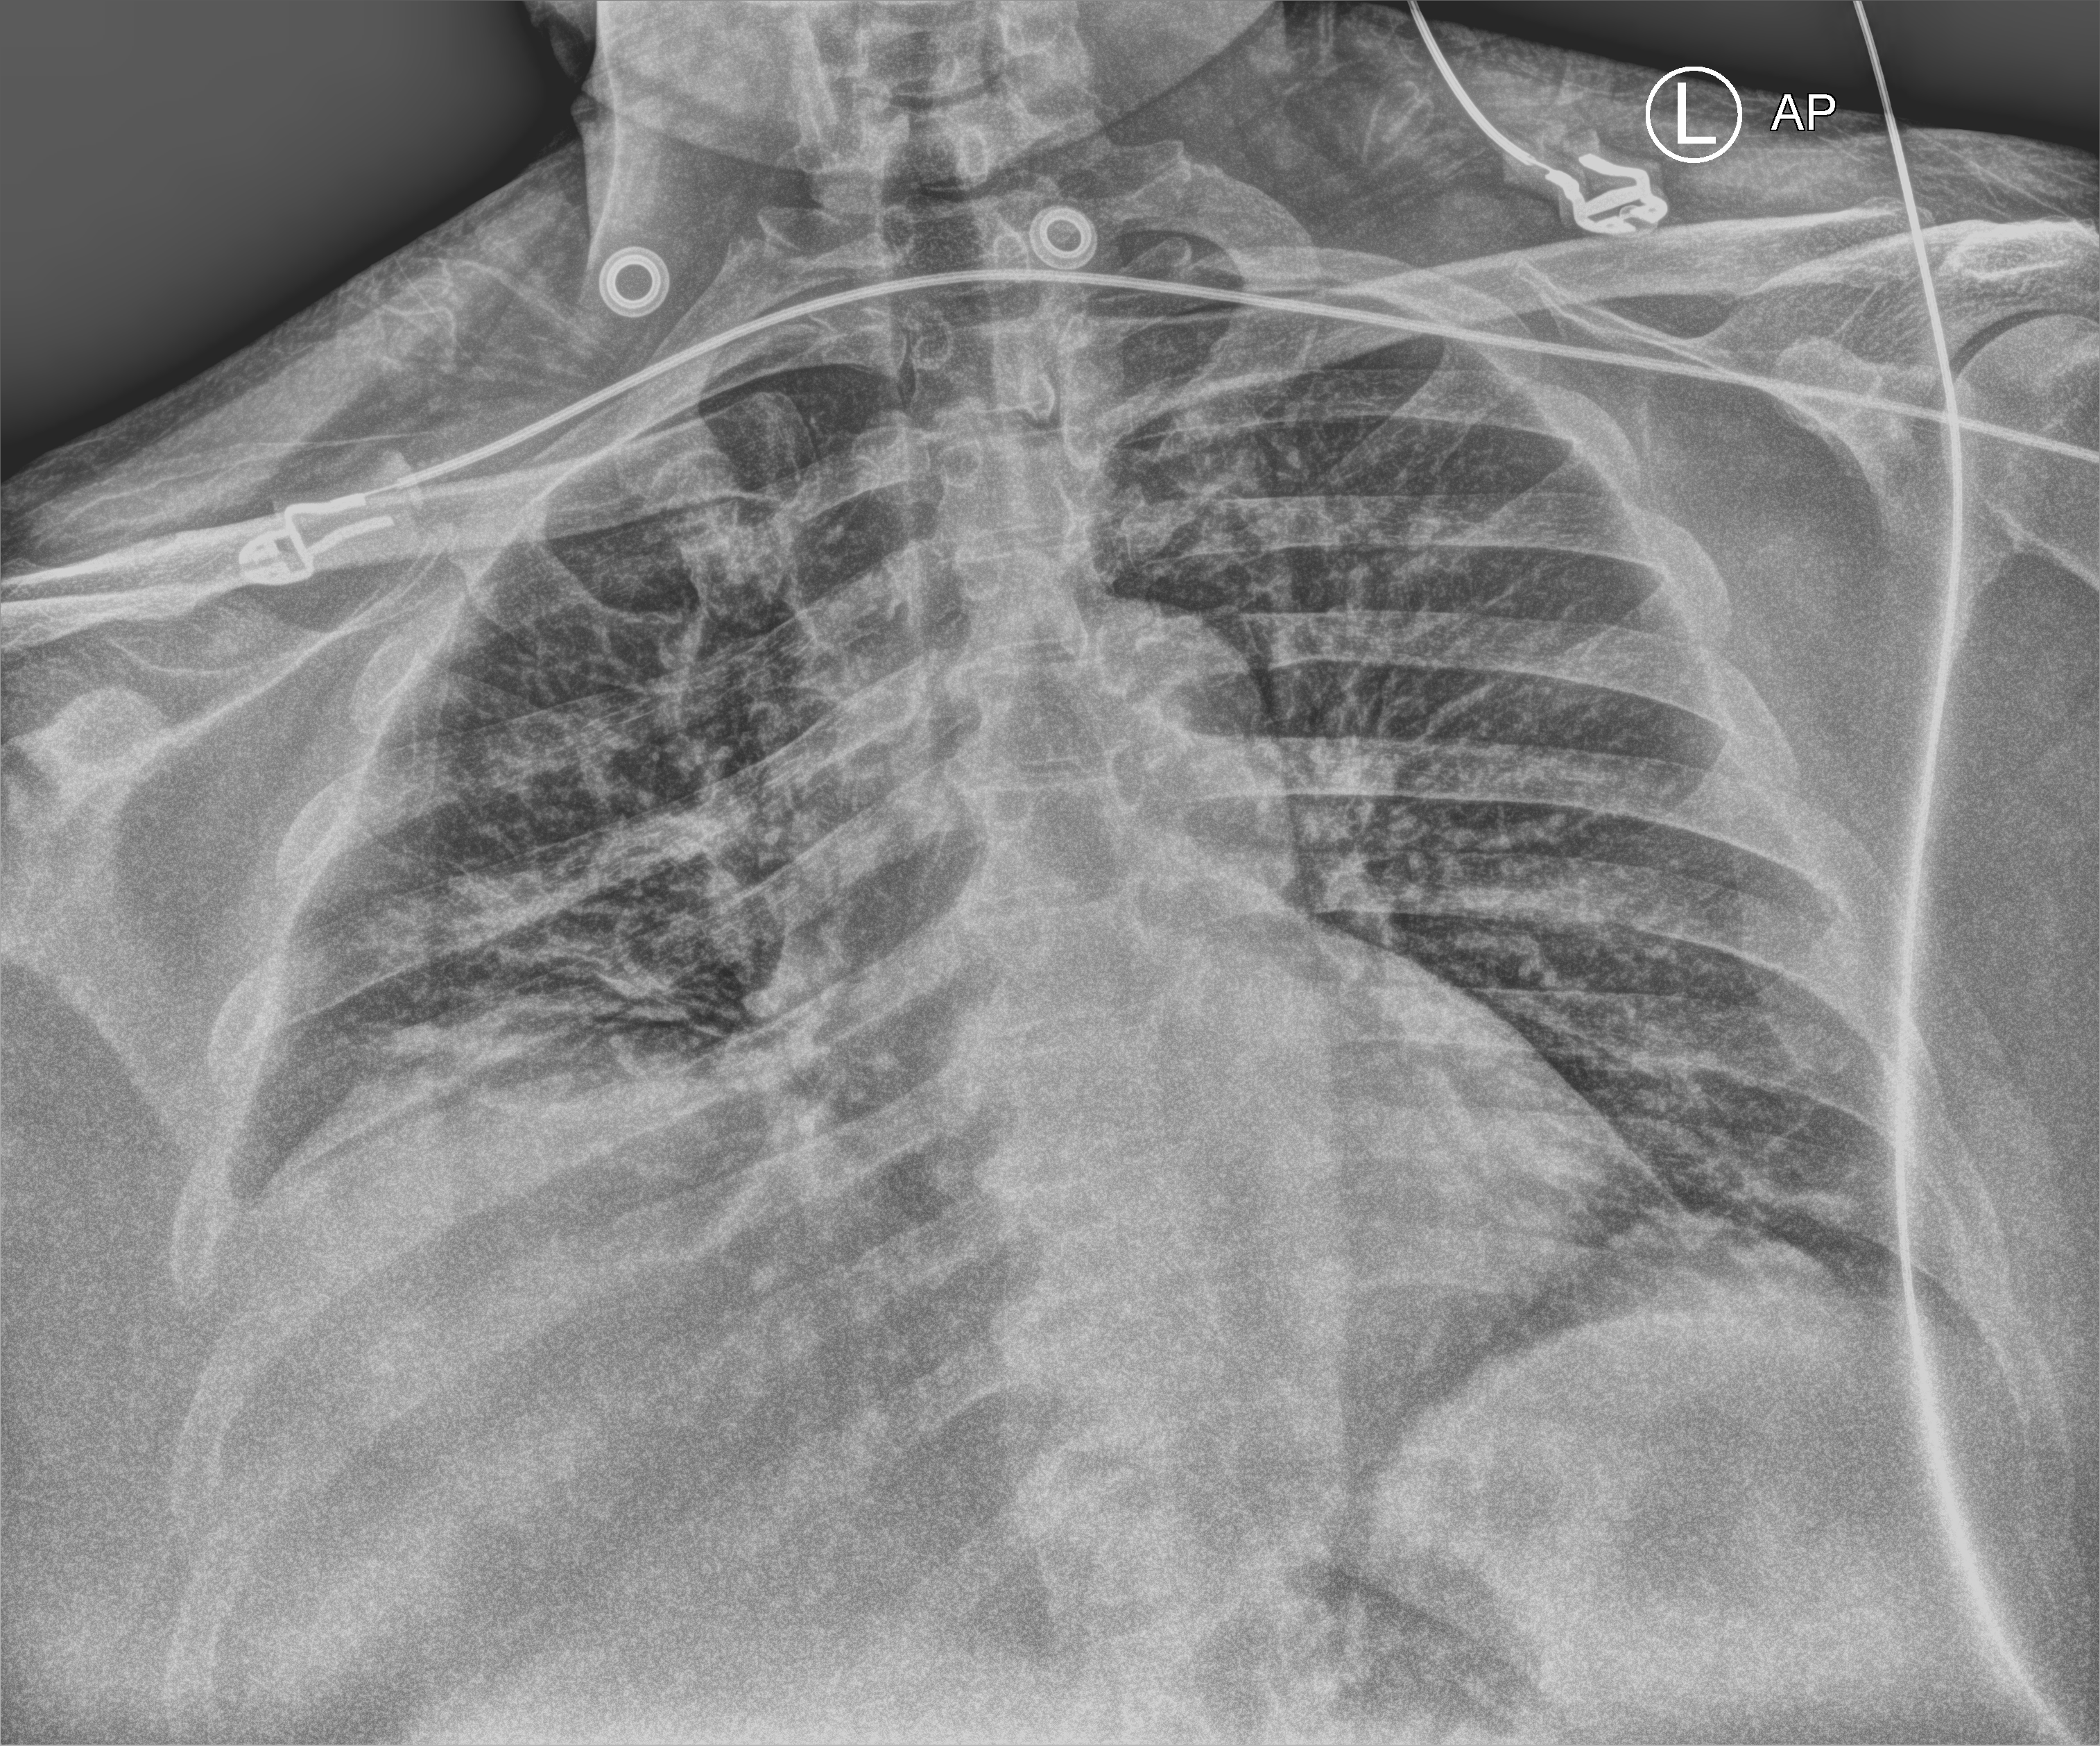
Bedside chest radiograph (computed radiography). Male patient hospitalised with COVID-19, age 18–59 years.
From the hospital-stay record, not from the radiograph (when in the stay this image was taken is not recorded):
- mechanically ventilated during this hospital stay: no